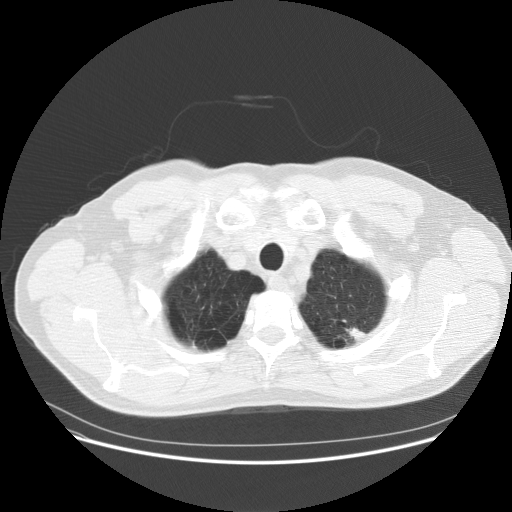
Axial slice from a low-dose chest CT screening exam. First (baseline) screen. Lung window (W 1500 / L -600 HU). 2.5 mm slice thickness. Slice 11 of 158 in the series. Male participant, aged 61 years at enrolment. Current smoker at enrolment.
- Lesion marked by an expert reader, box from (x=321, y=307) to (x=385, y=358) px.
- Screening reader's record for this exam (one nodule recorded; not confirmed to be the boxed lesion): non-calcified nodule or mass ≥4 mm, left upper lobe, 12 × 6 mm, poorly defined margins, soft tissue attenuation.
- Official screen result: positive, change unspecified: nodule(s) >= 4 mm or enlarging nodule(s), mass(es), or other non-specific abnormalities suspicious for lung cancer.
- Later outcome: lung cancer diagnosed 317 days after this screen — adenocarcinoma, NOS, left upper lobe, poorly differentiated (G3), stage IIIA (AJCC 6th edition), 30 mm at pathology.